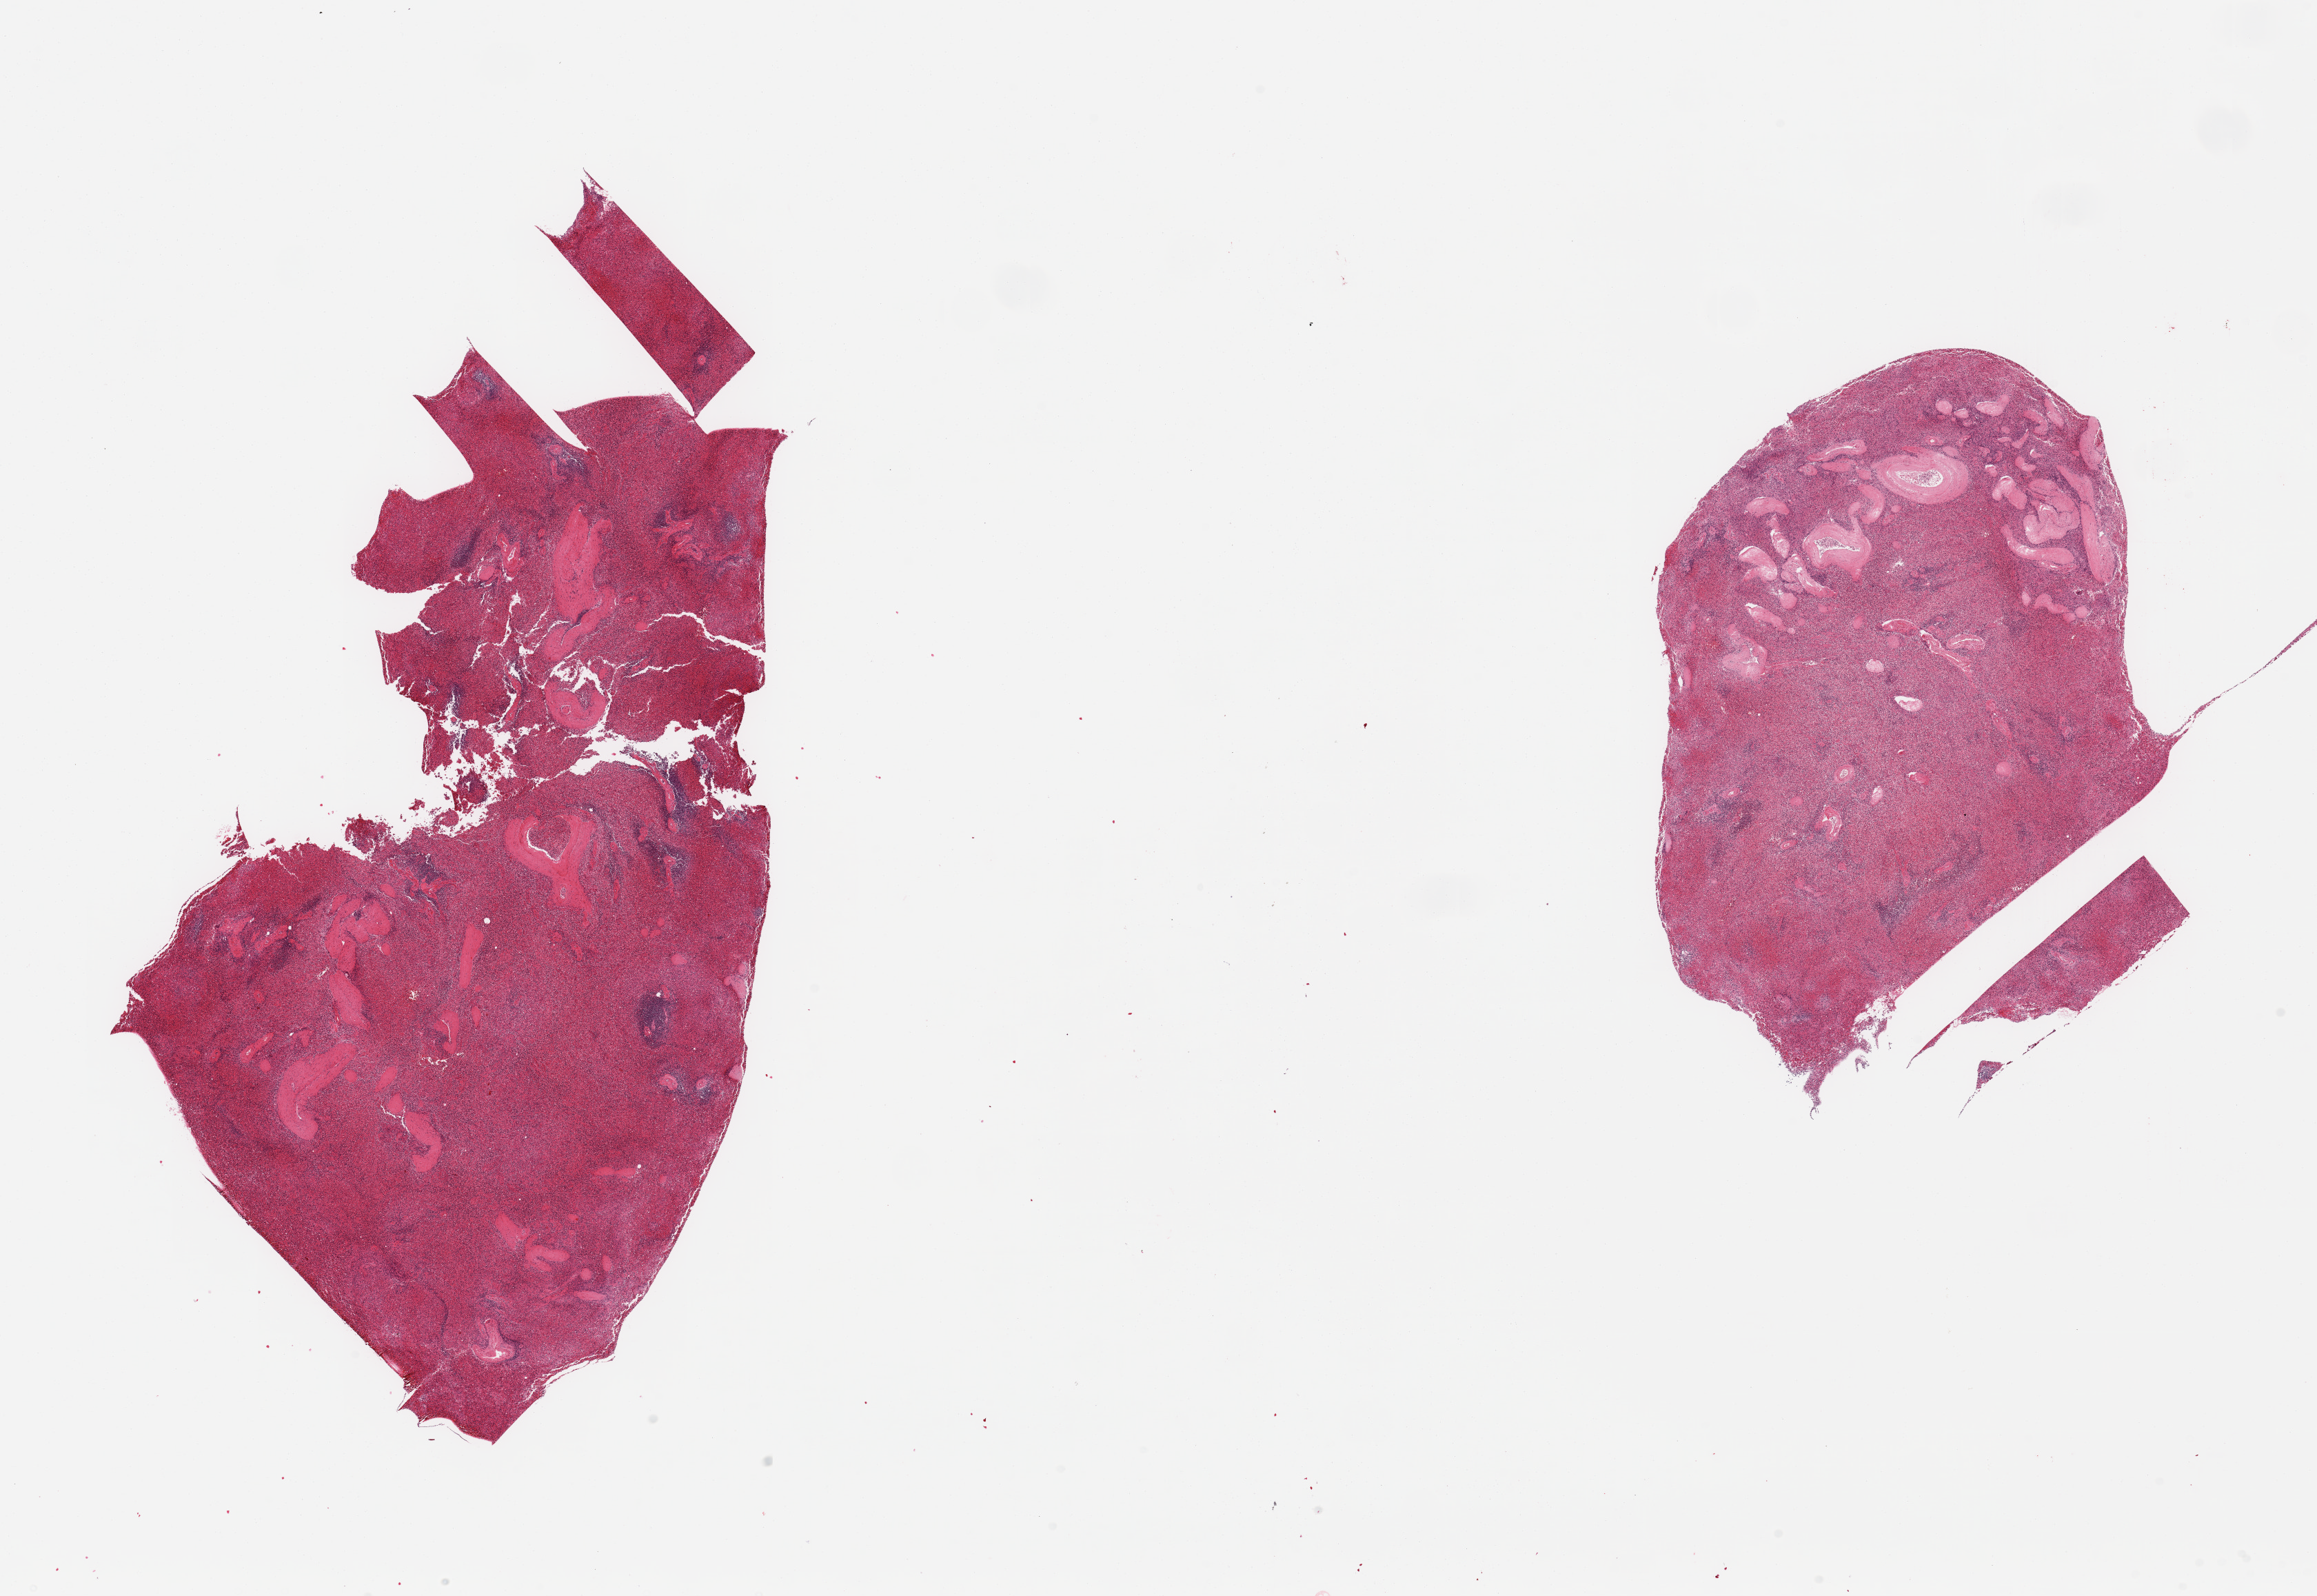
H&E whole-slide image, brightfield — whole scanned area (about 26.6 x 18.3 mm, acquisition: 20x scan) shown as a low-resolution overview, PAXgene-fixed, paraffin-embedded tissue, sampled site (target tissue): spleen, donor tissue sample. Donor sex: female.
Pathologist's review note for this sample: 2 pieces; minimal lymphoid content.